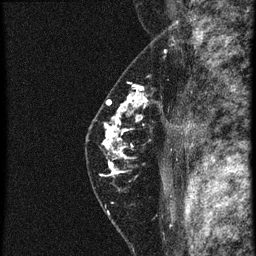
Breast MRI (dynamic contrast-enhanced), one sagittal slice; position 42 of 60 along the scan axis; 4 images stored at this slice position (order not interpretable as contrast timing); 1.5 T; TE 4.2 ms, TR 20.4 ms; 1.5 mm slice thickness; 256 × 256 image matrix, field of view 180 × 180 mm. Patient: female, 46 years. Case-level facts recorded for this patient, not image findings: setting: breast cancer imaged before/during neoadjuvant chemotherapy; receptor status: triple-negative.
Outlined on this slice (semi-automatically segmented with operator editing):
- analysis volume of interest (the breast-tissue region the enhancement analysis was run in; not a lesion): bounding box <88,82,181,185> (left, top, right, bottom; pixels)
- tumour enhancement mask (voxels above the 90 % enhancement threshold inside the analysis volume of interest): <104,92,147,175>